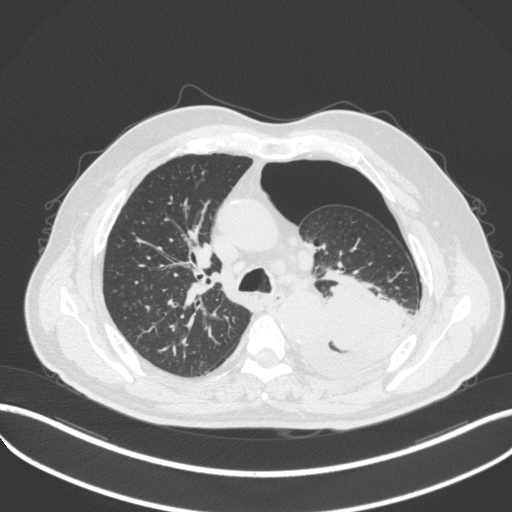
Chest CT, one axial slice. Position 347 of 466 along the scan axis. Reconstruction kernel B31f. Lung window (W 1500 / L -600 HU). 1 mm slice thickness. 512 × 512 image matrix, field of view 400 × 400 mm. Male patient, age 76 years. Case-level facts recorded for this patient, not image findings: clinical TNM (as recorded): T3 N0 M1b.
Outlined on this slice (bounding box drawn by a radiologist):
- lung tumour (recorded histology: adenocarcinoma): bounding box (x1, y1, x2, y2) in pixels: (294, 263, 412, 387)